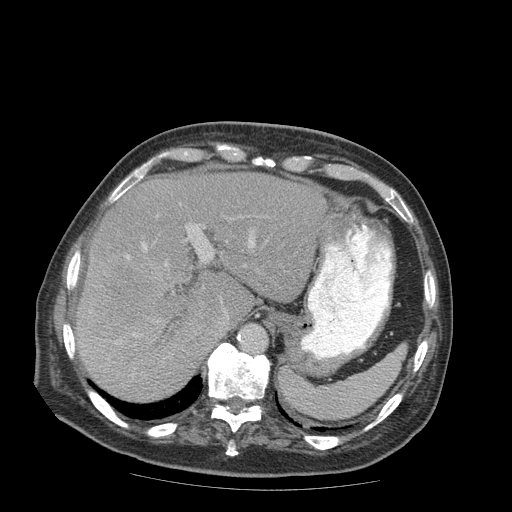
Contrast-enhanced abdominal CT (liver protocol), one axial slice. Slice 64 of 99 in the series (ordered by position). Soft-tissue window (W 400 / L 40 HU). 2.5 mm slice thickness. 512 × 512 image matrix. Case-level facts recorded for this patient, not image findings: diagnosis: hepatocellular carcinoma (patient treated with transarterial chemoembolisation; whether this scan precedes or follows treatment is not stated here); TNM stage (as recorded): Stage-IIIB; Child-Pugh class: A; tumour differentiation: well differentiated; tumour nodularity: multinodular.
Outlined on this slice (semi-automatic segmentation, software-assisted and operator-edited):
- liver parenchyma outside the tumour (the mass and vessels are separate outlines, so this box may not span the whole liver): bounding box [x1, y1, x2, y2] px = [76, 172, 326, 400]
- mass: [76, 245, 172, 343]
- liver vessels: [126, 225, 255, 337]